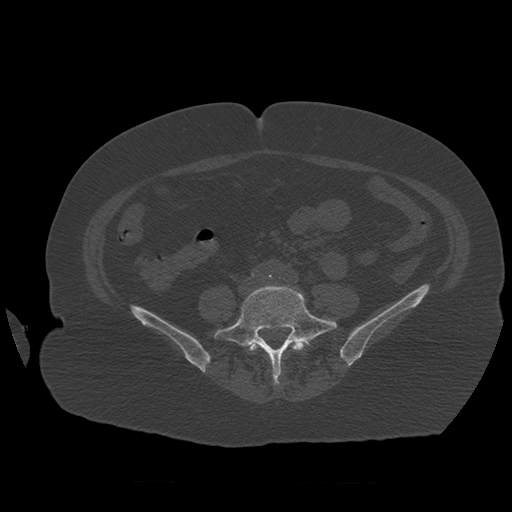
CT including the spine, one axial slice; slice 188 of 399 in the series (ordered by position); reconstruction kernel STANDARD; bone window (W 1800 / L 400 HU); 1.25 mm slice thickness; 512 × 512 image matrix. Patient age 81 years. From the clinical record (not read from this slice): primary cancer: renal; vertebrae with lytic lesions (as recorded): L1.
Annotated regions visible in this slice (semi-automatic segmentation, software-assisted and operator-edited):
- L4 vertebra: bounding box [x1, y1, x2, y2] px = [249, 338, 308, 380]
- L5 vertebra: [214, 285, 337, 385]